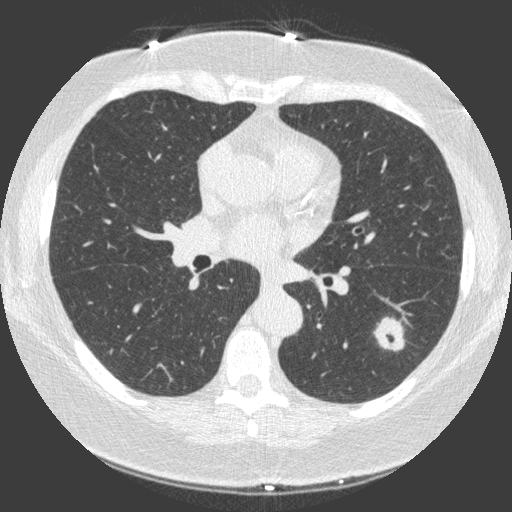
Low-dose screening chest CT, one axial slice. Slice 86 of 149 in the series (ordered by position). 120 kVp. Lung window (W 1500 / L -600 HU). 1 mm slice thickness. 512 × 512 image matrix, field of view 330 × 330 mm.
Outlined on this slice (expert manual segmentation):
- lesion 1 (tumor, lower lobe of left lung): bounding box <374,317,404,351> (left, top, right, bottom; pixels)